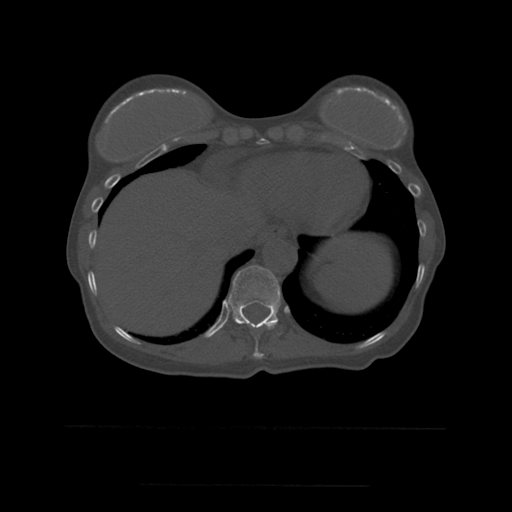
CT including the spine, one axial slice. Slice 289 of 544 in the series (ordered by position). Bone window (W 1800 / L 400 HU). 512 × 512 image matrix. Patient age 58 years. Case-level facts recorded for this patient, not image findings: primary cancer: lung.
Structures marked on this image (semi-automatically segmented with operator editing):
- T10 vertebra: bounding box <242,321,278,359> (left, top, right, bottom; pixels)
- T11 vertebra: <226,266,281,324>